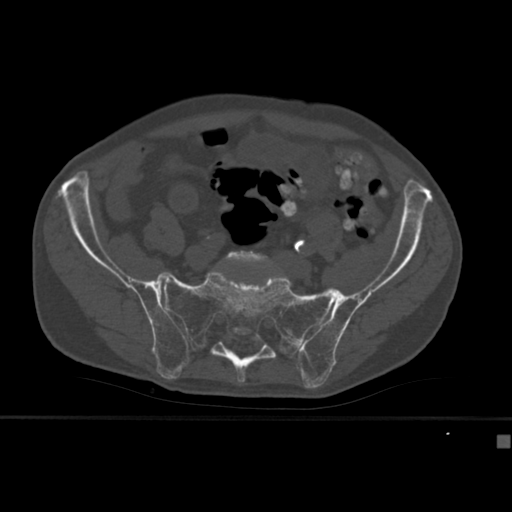
CT including the spine, one axial slice. Slice 67 of 430 in the series (ordered by position). 120 kVp. Bone window (W 1800 / L 400 HU). 512 × 512 image matrix, field of view 337 × 337 mm. Patient: male, 64 years. From the clinical record (not read from this slice): primary cancer: uterus.
Structures marked on this image (semi-automatically segmented with operator editing):
- L5 vertebra: bounding box (x1, y1, x2, y2) in pixels: (220, 251, 275, 269)